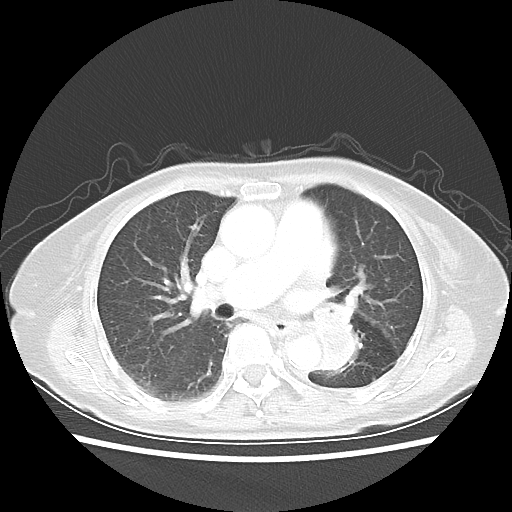
Chest CT, one axial slice; position 28 of 50 along the scan axis; reconstruction kernel LUNG; lung window (W 1500 / L -600 HU); 512 × 512 image matrix, field of view 335 × 335 mm. Patient: female, 81 years. From the clinical record (not read from this slice): clinical TNM (as recorded): T2 N0 M1a.
Outlined on this slice (rectangle marked by the reading radiologist):
- lung tumour (recorded histology: squamous cell carcinoma): box from (x=304, y=302) to (x=369, y=377) px